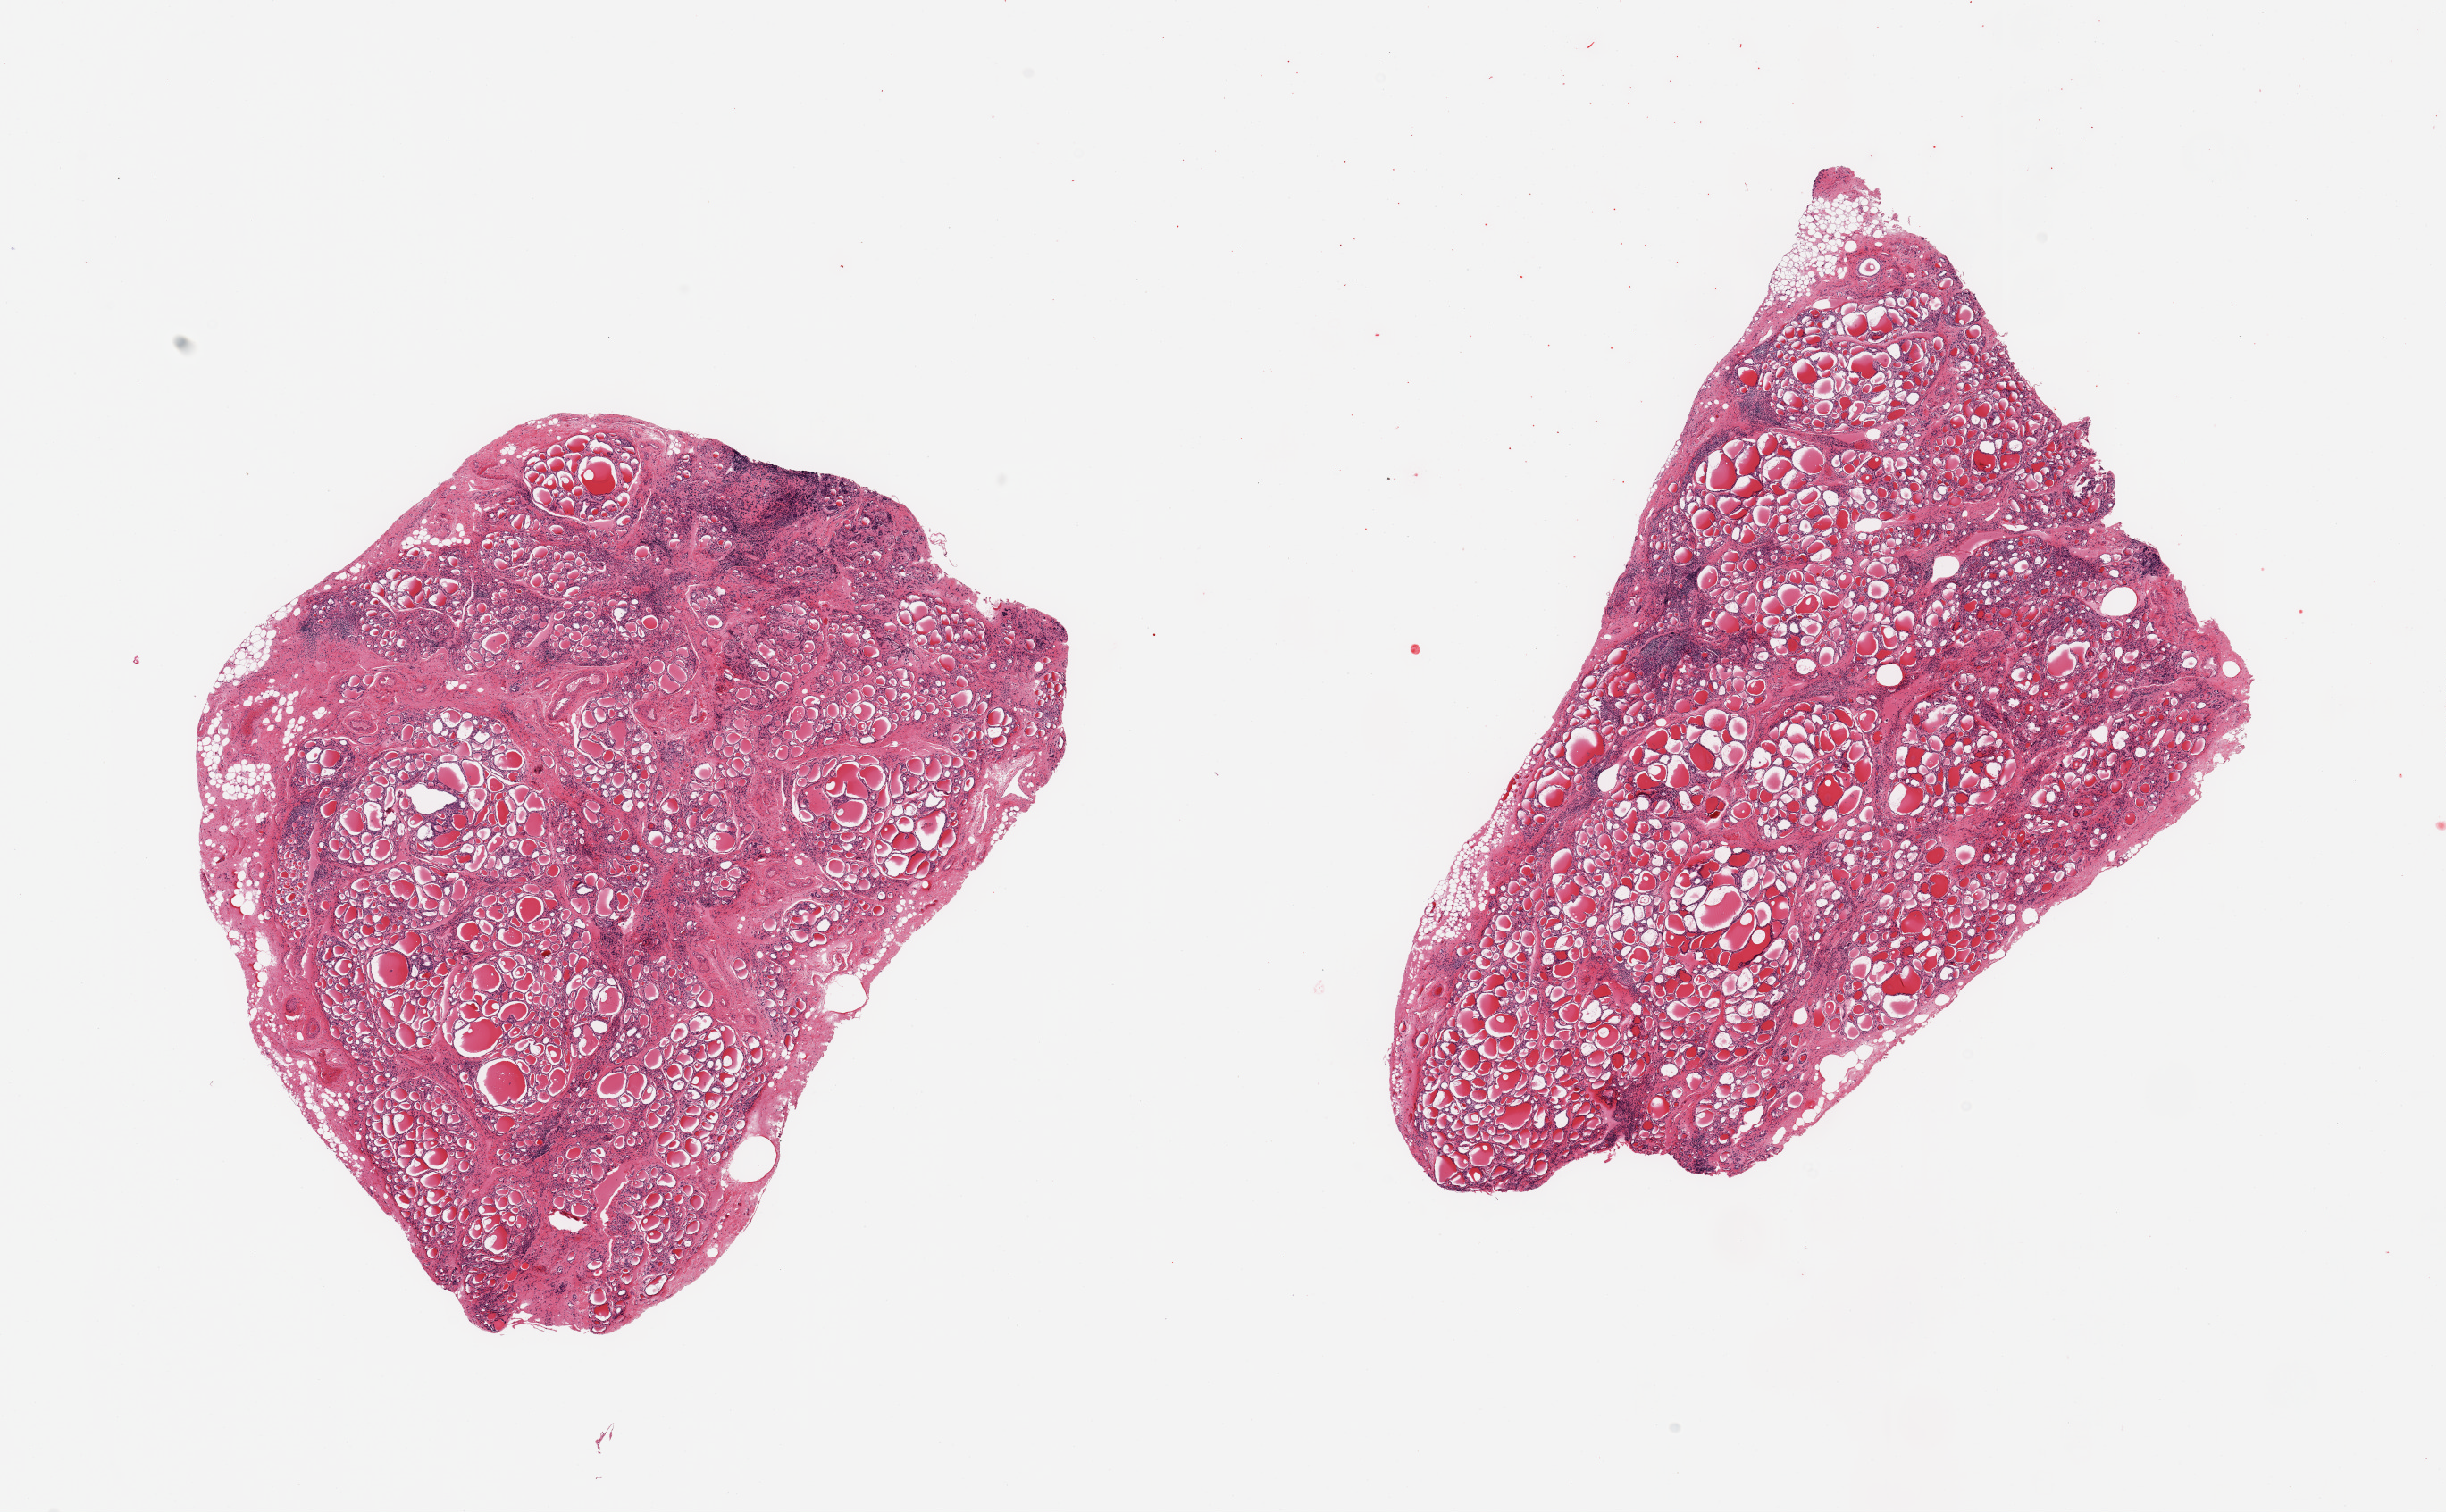
Digitized hematoxylin and eosin (H&E)-stained section — whole scanned area (about 21.7 x 13.4 mm, from a 20x scan) shown as a low-resolution overview; PAXgene-fixed paraffin-embedded (PFPE) section; section of thyroid (target tissue); donor tissue sample. Female donor.
Review note (as recorded): 2 pieces; Hashimoto thyroiditis with slight lymphocytic and moderate fibrous increase.